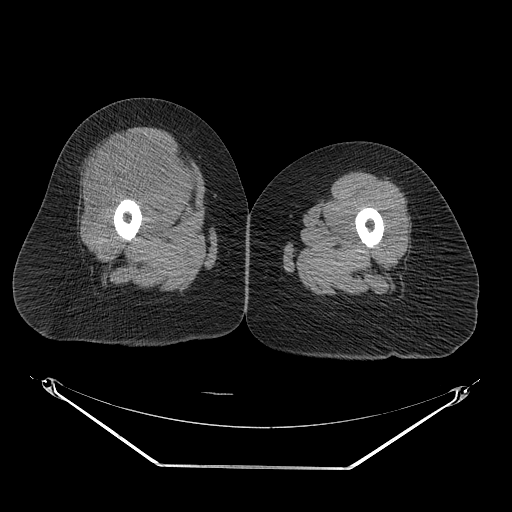
CT of an extremity soft-tissue mass (from a PET/CT study), one axial slice; slice 31 of 267 in the series (ordered by position); reconstruction kernel STANDARD; 140 kVp; soft-tissue window (W 400 / L 40 HU); 3.75 mm slice thickness; 512 × 512 image matrix, field of view 500 × 500 mm. Female patient. Case-level facts recorded for this patient, not image findings: histological type: malignant solitary fibrous tumor; grade: intermediate; site of the primary tumour: right thigh.
Outlined on this slice (expert contour drawn on MRI and transferred to this co-registered scan by the dataset authors):
- gross tumour volume including surrounding oedema: bounding box <94,132,204,220> (left, top, right, bottom; pixels)
- gross tumour volume (mass): <100,132,200,216>